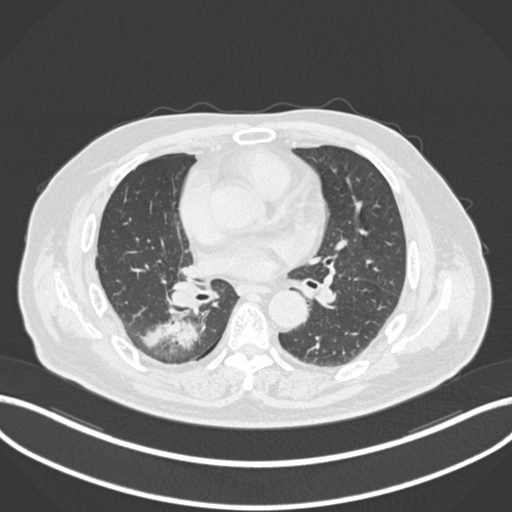
Chest CT, one axial slice; position 93 of 218 along the scan axis; reconstruction kernel B30f; 120 kVp; lung window (W 1500 / L -600 HU); 1 mm slice thickness; 512 × 512 image matrix. Male patient, age 68 years. From the clinical record (not read from this slice): clinical TNM (as recorded): T2a N0 M0.
Annotated regions visible in this slice (rectangle marked by the reading radiologist):
- lung tumour (recorded histology: adenocarcinoma): bounding box <137,311,199,353> (left, top, right, bottom; pixels)